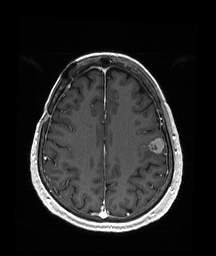
Brain MRI from a brain-tumour surgery series, one axial slice; position 66 of 176 along the scan axis; T1-weighted post-contrast; 216 × 256 image matrix, field of view 211 × 250 mm. Case-level facts recorded for this patient, not image findings: histopathology: Metastatic Malignant Melanoma.
Outlined on this slice (manually delineated by an expert):
- tumour: bounding box <148,138,165,153> (left, top, right, bottom; pixels)